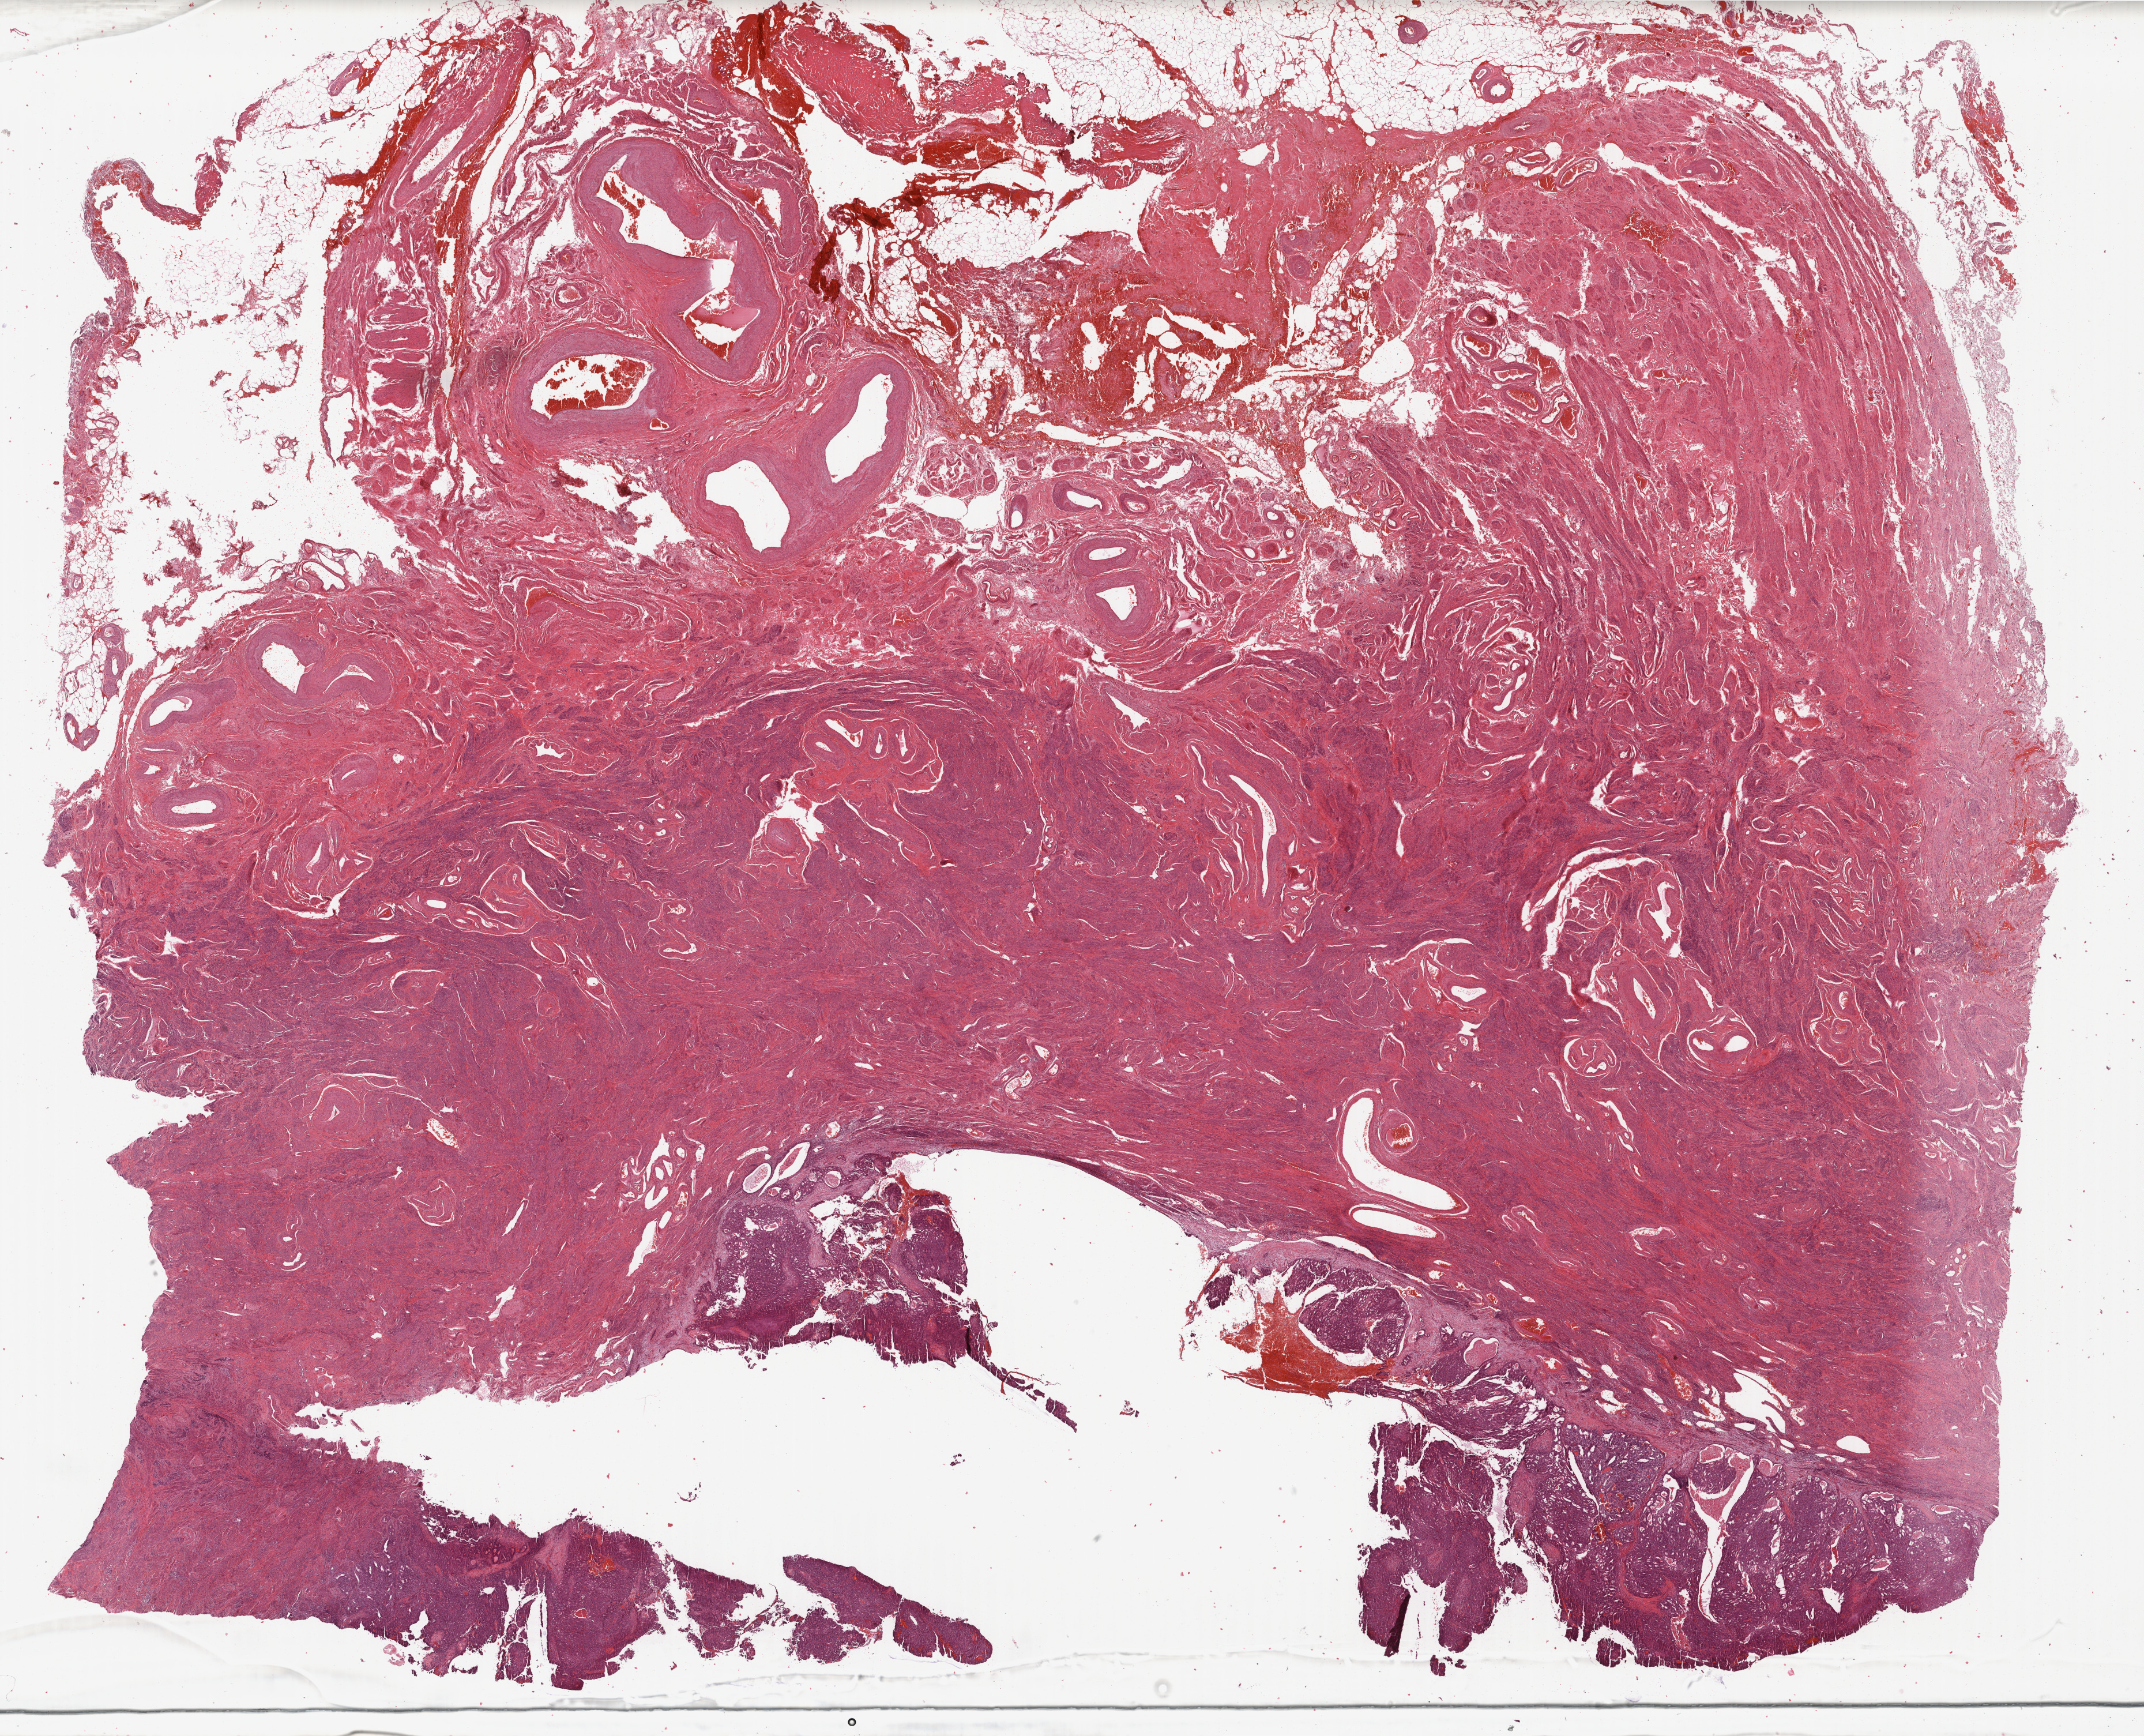
Digitized H&E-stained tissue section (whole slide), shown as a low-resolution overview of the whole scanned area (about 29.5 x 23.9 mm, acquisition: 40x scan). FFPE section. Primary tumour sample from the uterus. Female patient; age at initial diagnosis 62 years.
Diagnosis: Endometrioid adenocarcinoma, NOS.